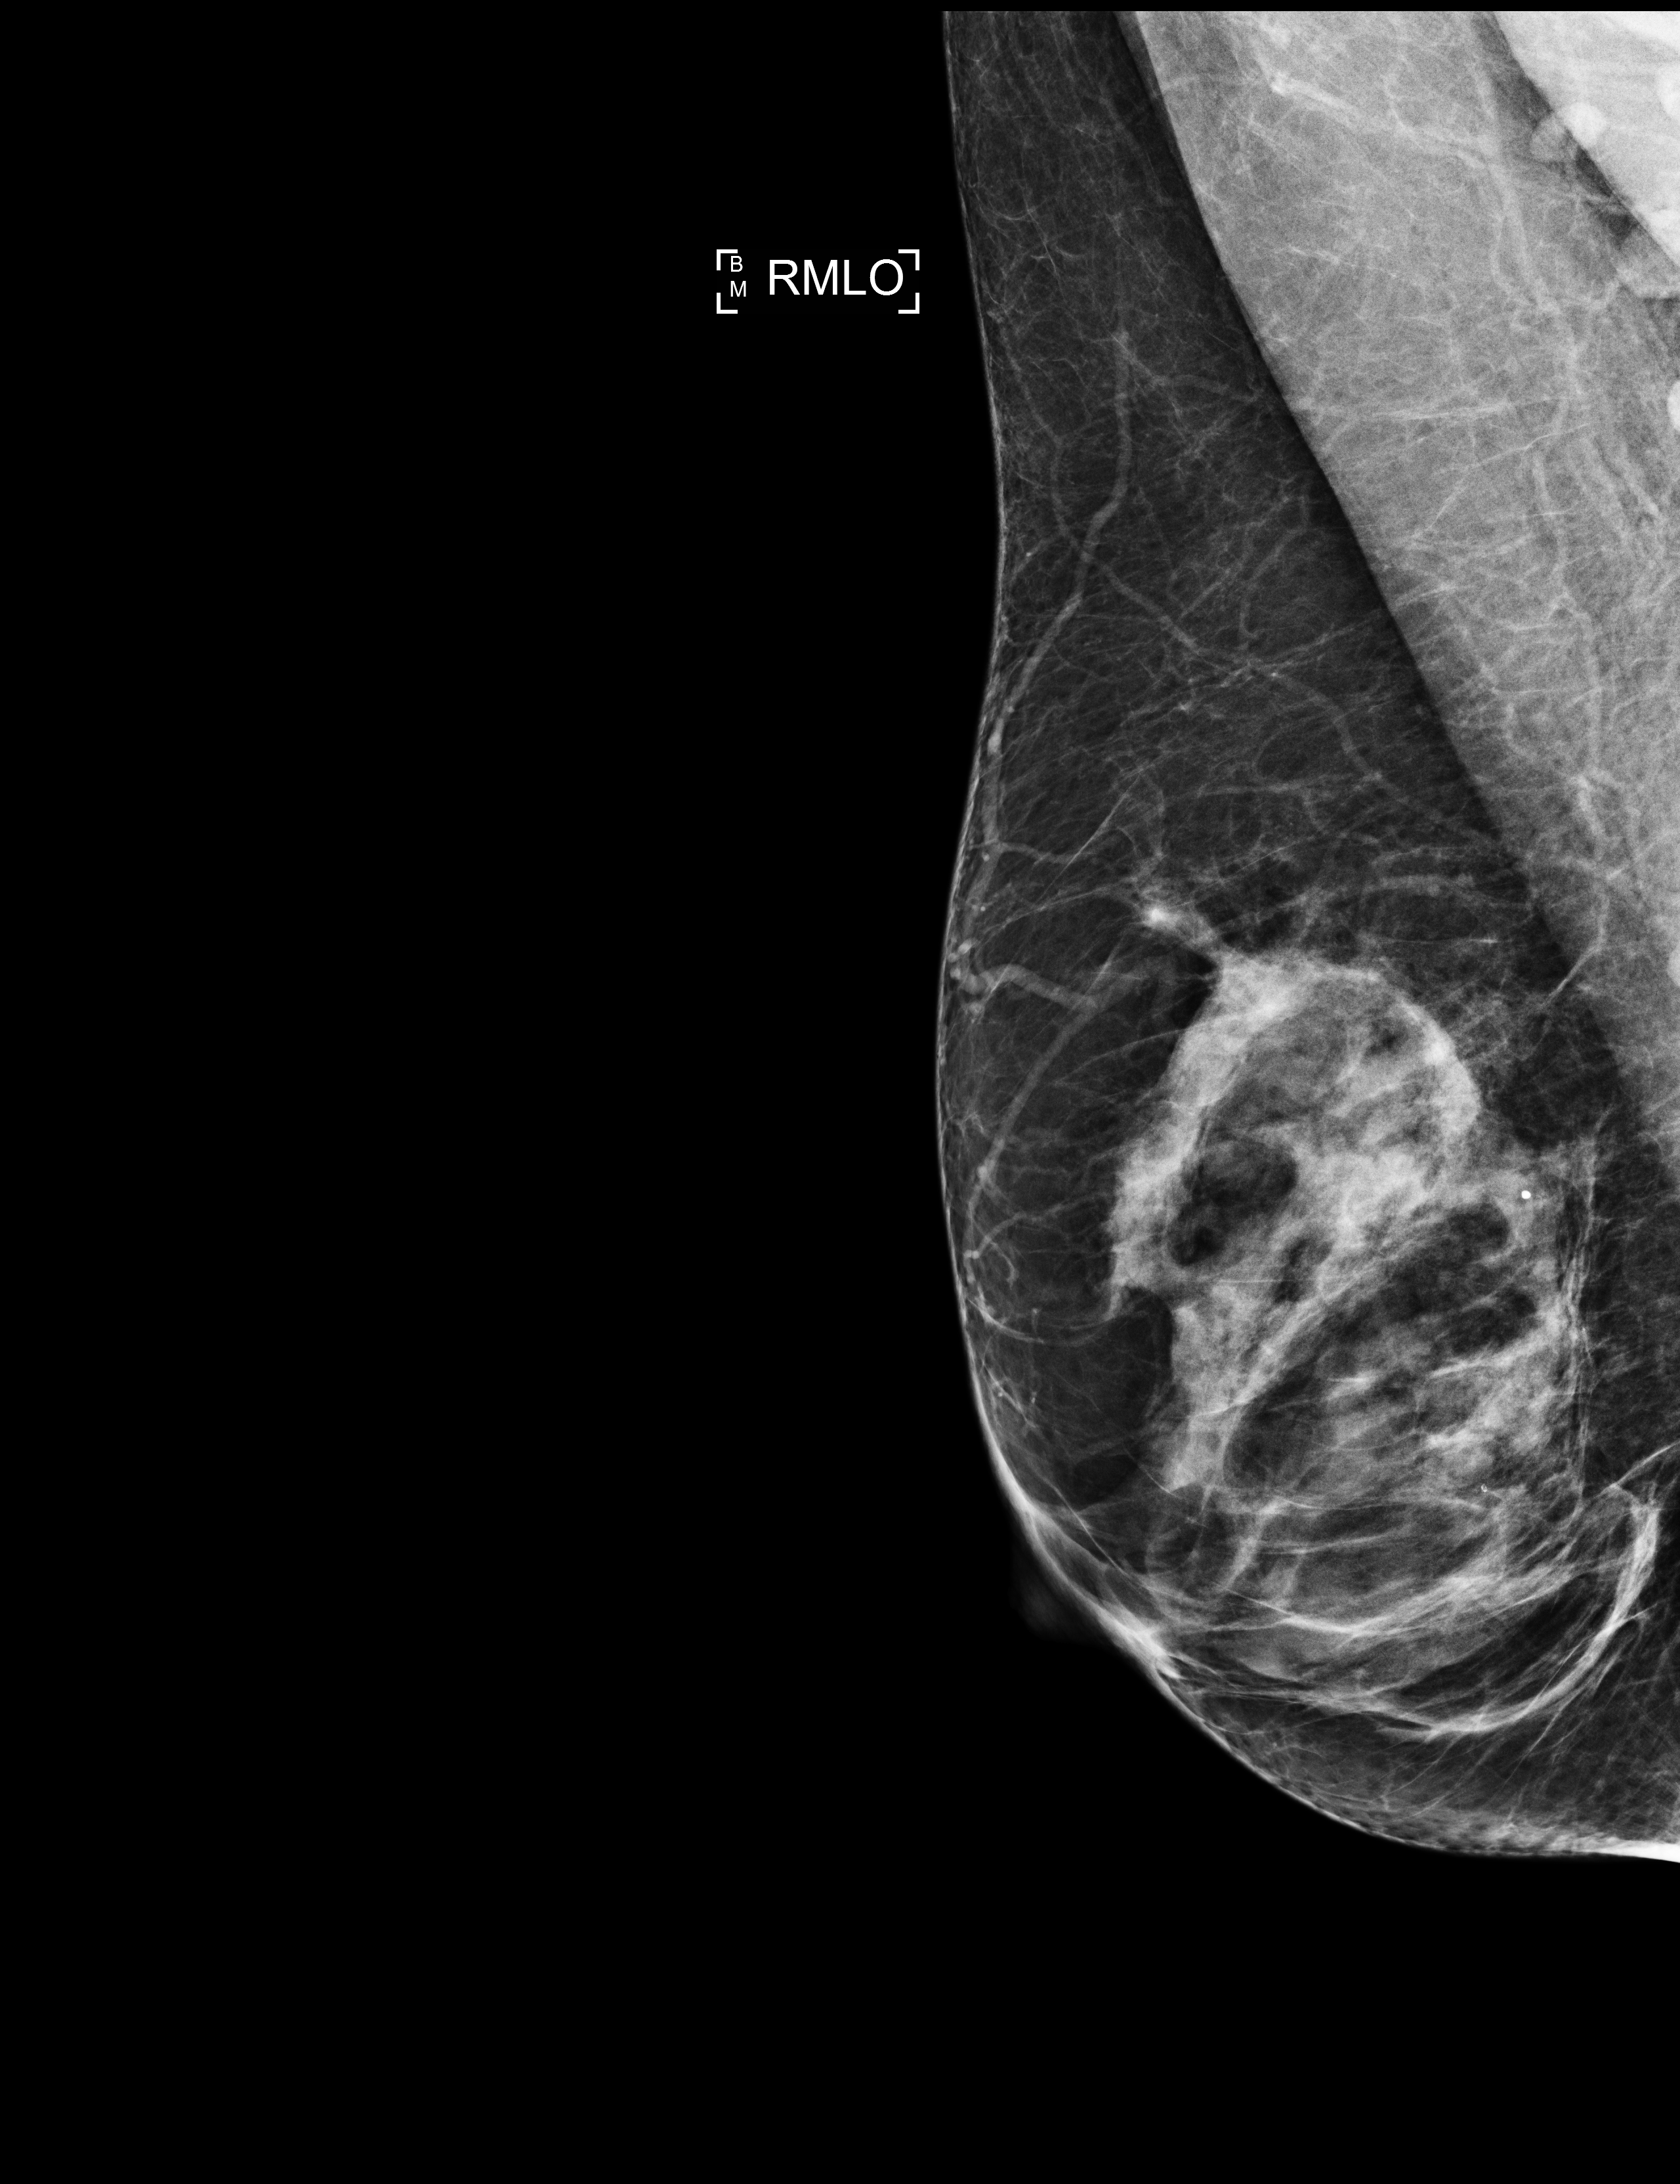
Screening examination; compressed breast thickness 62 mm. Patient: female, 60 years.
Image type: full-field digital mammogram. Breast: right. Projection: MLO view.